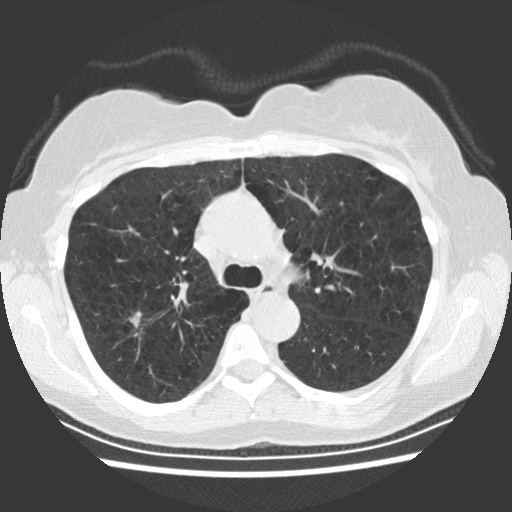
Axial slice from a low-dose chest CT screening exam; first (baseline) screen; lung window (W 1500 / L -600 HU); slice 75 of 234 in the series. Female participant, aged 66 years at enrolment.
- Expert-annotated lung lesion, bounding box [x1, y1, x2, y2] px = [110, 303, 153, 341].
- The exam's reader record, not a measurement of the box and not confirmed to be the same lesion: non-calcified nodule or mass ≥4 mm, right upper lobe, 10 × 8 mm, smooth margins, soft tissue attenuation.
- Official screen result: positive, change unspecified: nodule(s) >= 4 mm or enlarging nodule(s), mass(es), or other non-specific abnormalities suspicious for lung cancer.
- Later outcome: lung cancer diagnosed 54 days after this screen — squamous cell carcinoma, keratinizing, NOS, right upper lobe, poorly differentiated (G3), stage IA (AJCC 6th edition), 11 mm at pathology.